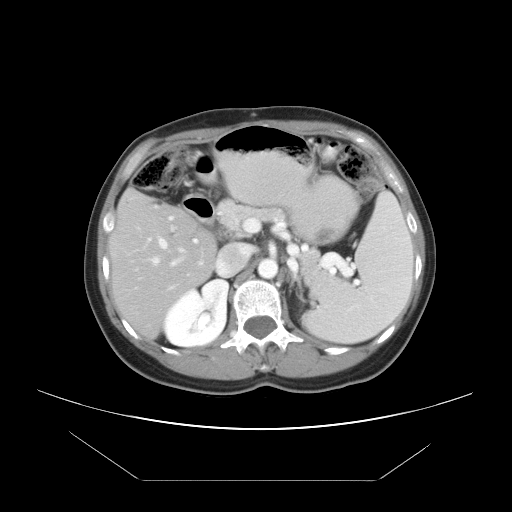
Contrast-enhanced abdominal CT, one axial slice; slice 25 of 45 in the series (ordered by position); reconstruction kernel STANDARD; soft-tissue window (W 400 / L 40 HU); 5 mm slice thickness; 512 × 512 image matrix, field of view 405 × 405 mm. Female patient, age 52 years. Case-level facts recorded for this patient, not image findings: diagnosis: colorectal cancer liver metastases, imaged before liver resection; multiple liver metastases: yes; largest metastasis: 2.5 cm; disease in both lobes: no.
Structures marked on this image (manually delineated by an expert):
- hepatic veins: box from (x=154, y=239) to (x=178, y=266) px
- liver: (x=112, y=192)–(x=215, y=337)
- planned liver remnant (the part of the liver to remain after resection): (x=112, y=193)–(x=215, y=337)
- portal vein (with intrahepatic branches): (x=147, y=216)–(x=198, y=289)